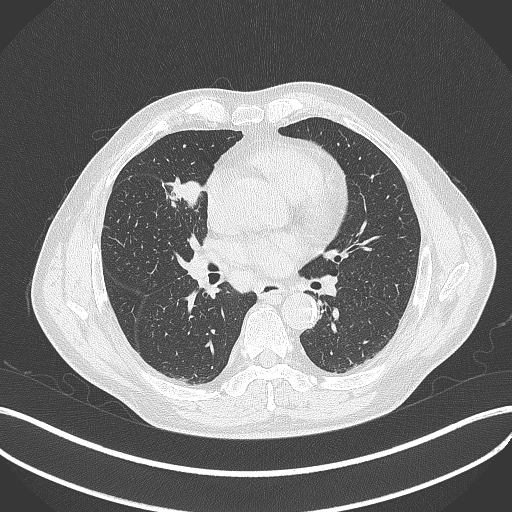
Chest CT, one axial slice; position 202 of 429 along the scan axis; 120 kVp; lung window (W 1500 / L -600 HU); 1 mm slice thickness; 512 × 512 image matrix, field of view 400 × 400 mm. Patient: male, 61 years. From the clinical record (not read from this slice): clinical TNM (as recorded): T2b N1 M0.
Structures marked on this image (rectangle marked by the reading radiologist):
- lung tumour (recorded histology: squamous cell carcinoma): bounding box (x1, y1, x2, y2) in pixels: (170, 175, 202, 209)